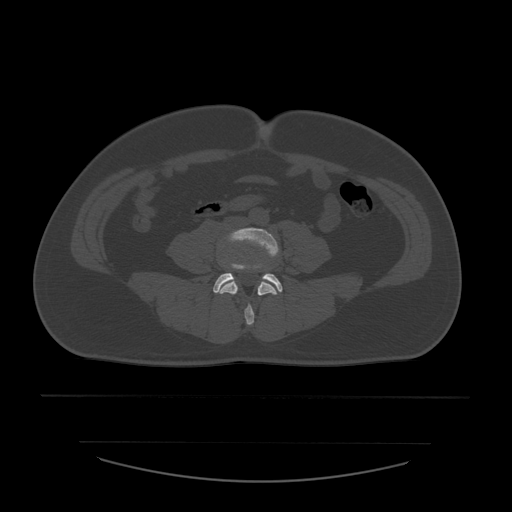
CT including the spine, one axial slice. Position 135 of 532 along the scan axis. Reconstruction kernel STANDARD. Bone window (W 1800 / L 400 HU). 1.25 mm slice thickness. 512 × 512 image matrix. Patient age 44 years. From the clinical record (not read from this slice): primary cancer: soft tissue sarcoma.
Annotated regions visible in this slice (semi-automatically segmented with operator editing):
- L4 vertebra: bounding box [x1, y1, x2, y2] px = [216, 228, 280, 325]
- L5 vertebra: [213, 264, 283, 293]